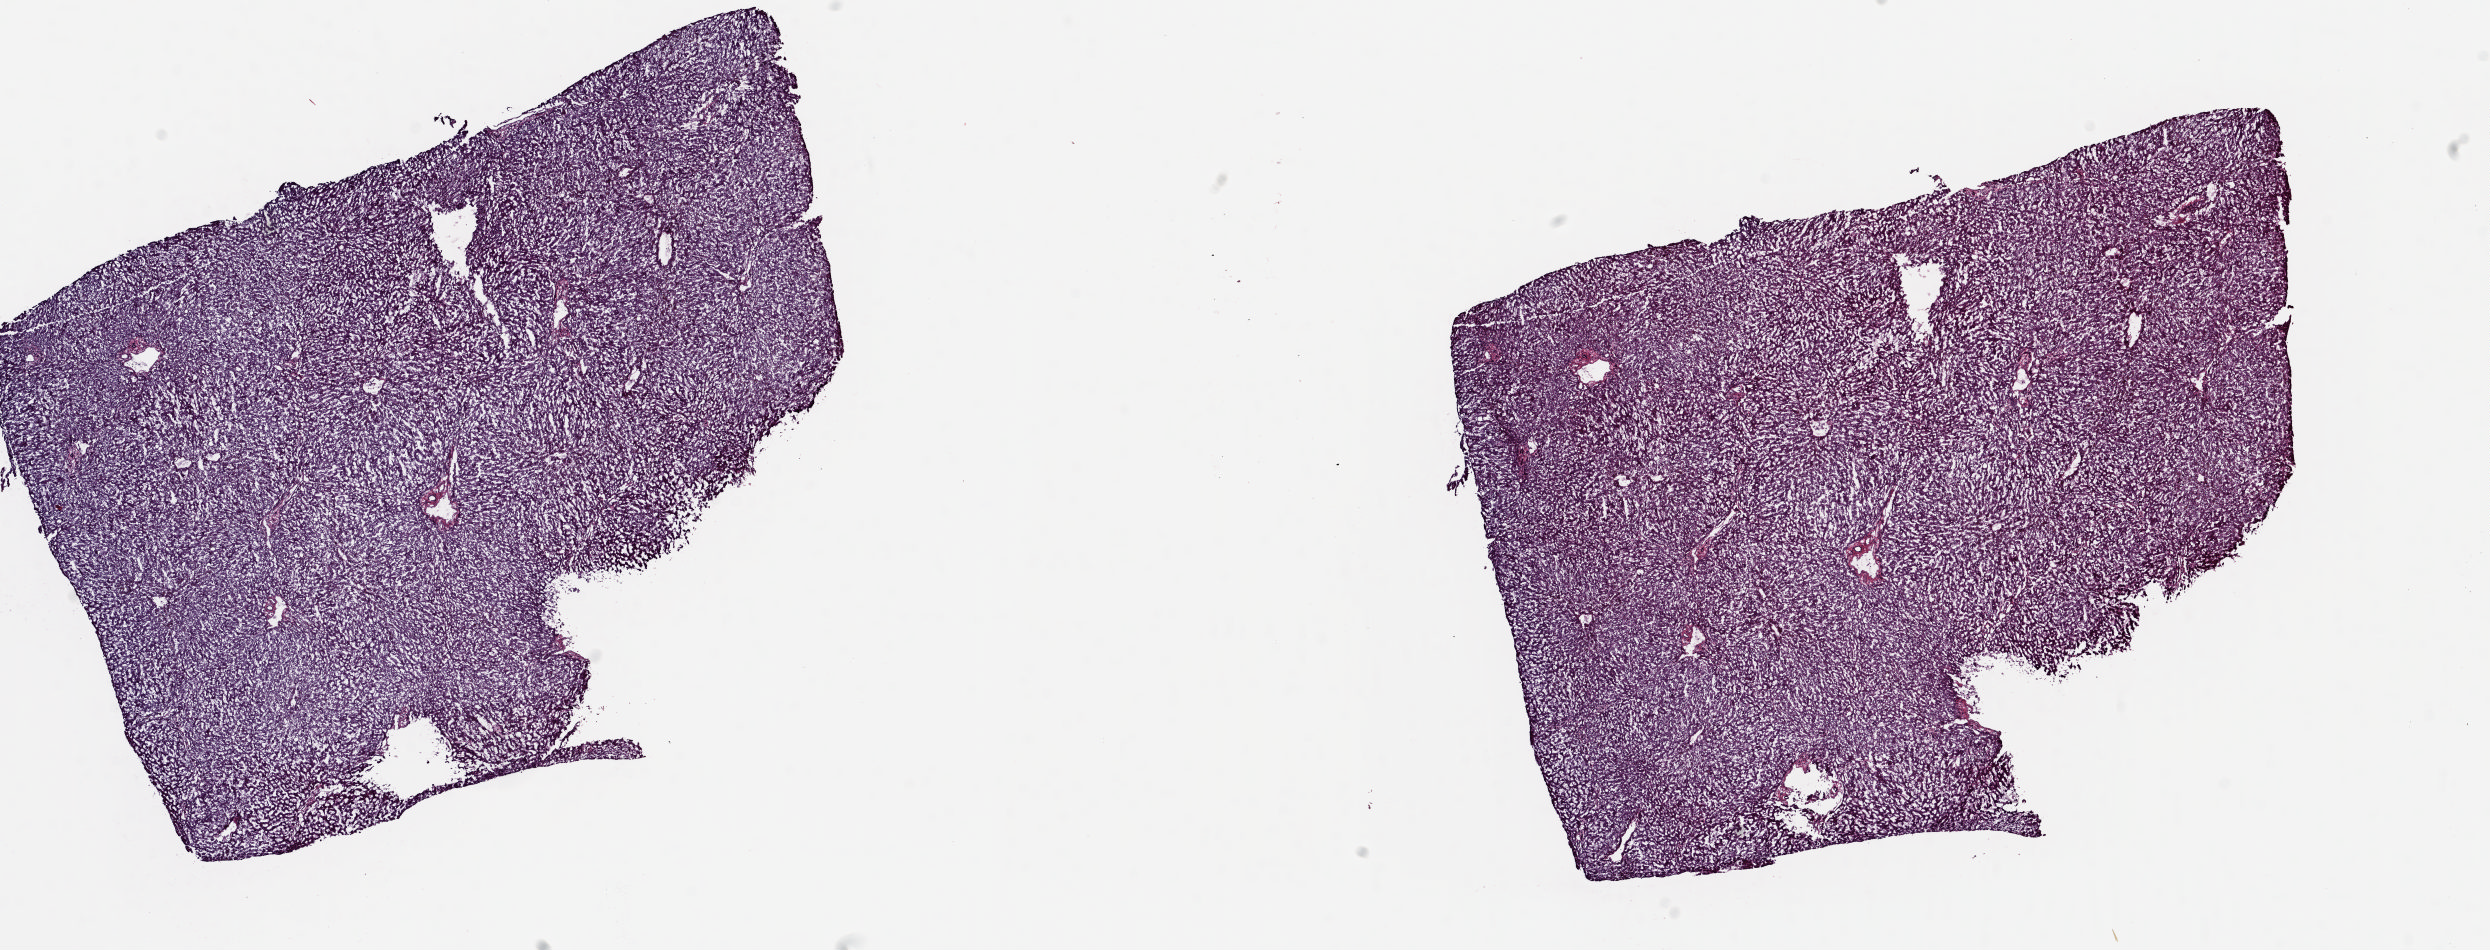
H&E-stained whole-slide image, whole scanned area (about 19.8 x 7.5 mm, acquisition: 20x scan) shown as a low-resolution overview; frozen section; liver, solid tissue normal (non-tumour tissue) sample. Female, age 55 years at initial diagnosis. Slide review estimates, as recorded: tumour cells 0%, tumour nuclei 0%, normal cells 95%, stromal cells 5%, necrosis 0%. Infiltration values recorded for this section: lymphocyte infiltration 1%, monocyte infiltration 0%, neutrophil infiltration 0%.
This section: solid tissue normal (non-tumour) sample from the same patient. Patient diagnosis: Hepatocellular carcinoma, NOS.